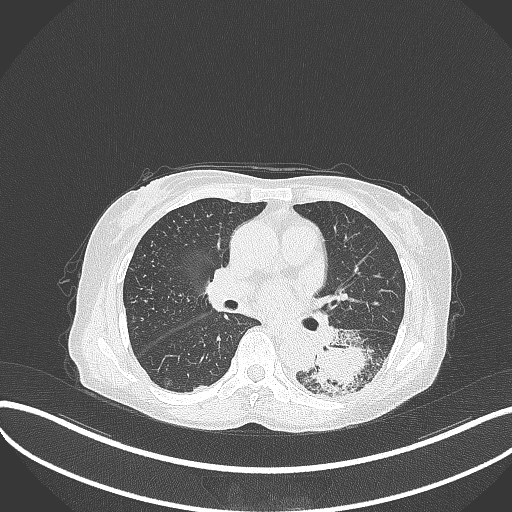
Chest CT, one axial slice; reconstruction kernel B70f; lung window (W 1500 / L -600 HU); 512 × 512 image matrix. Female patient, age 78 years. From the clinical record (not read from this slice): clinical TNM (as recorded): T3 N0 M1.
Structures marked on this image (rectangle marked by the reading radiologist):
- lung tumour (recorded histology: squamous cell carcinoma): box from (x=303, y=328) to (x=382, y=398) px